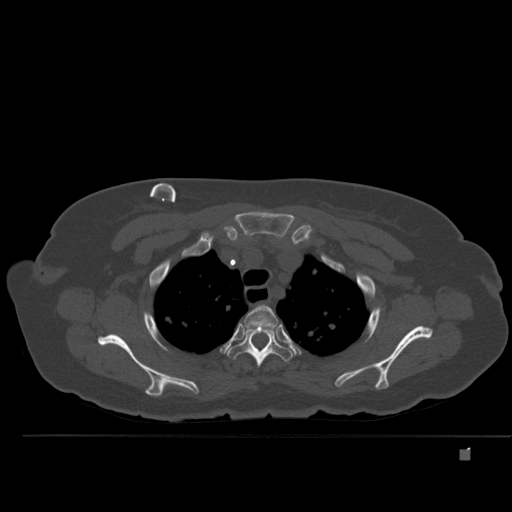
CT including the spine, one axial slice. Bone window (W 1800 / L 400 HU). 1.5 mm slice thickness. 512 × 512 image matrix. Patient: female, 74 years. From the clinical record (not read from this slice): primary cancer: colon.
Annotated regions visible in this slice (semi-automatically segmented with operator editing):
- T2 vertebra: bounding box (x1, y1, x2, y2) in pixels: (244, 305, 278, 328)
- T3 vertebra: (227, 325, 294, 367)